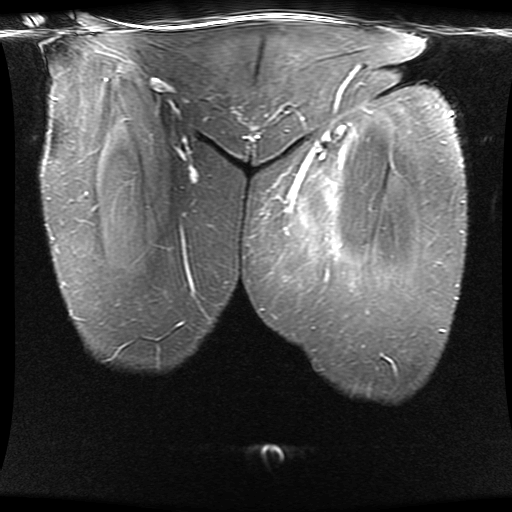
MRI of an extremity soft-tissue mass, one coronal slice; slice 4 of 30 in the series (ordered by position); STIR; 512 × 512 image matrix, field of view 460 × 460 mm. Female patient. From the clinical record (not read from this slice): histological type: myxofibrosarcoma; grade: intermediate; site of the primary tumour: left thigh.
Structures marked on this image (manually delineated by an expert):
- gross tumour volume including surrounding oedema: bounding box [x1, y1, x2, y2] px = [302, 190, 330, 223]
- gross tumour volume (mass): [302, 190, 330, 223]